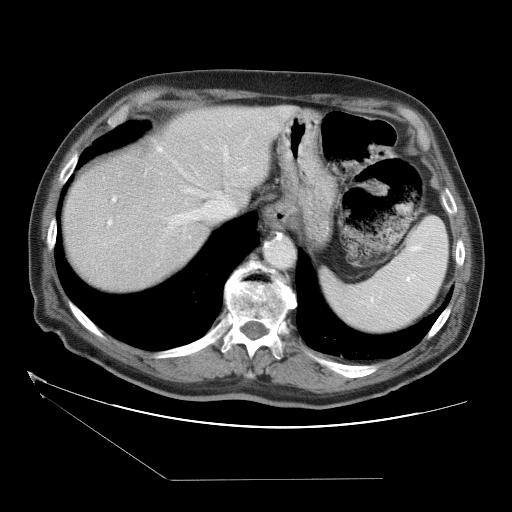
Contrast-enhanced abdominal CT (liver protocol), one axial slice. Slice 28 of 38 in the series (ordered by position). Reconstruction kernel STANDARD. One of 2 acquisitions stored at this slice position. Soft-tissue window (W 400 / L 40 HU). 5 mm slice thickness. 512 × 512 image matrix. Case-level facts recorded for this patient, not image findings: diagnosis: hepatocellular carcinoma (patient treated with transarterial chemoembolisation; whether this scan precedes or follows treatment is not stated here); TNM stage (as recorded): Stage-II; Child-Pugh class: A; tumour nodularity: multinodular.
Outlined on this slice (semi-automatically segmented with operator editing):
- abdominal aorta: bounding box (x1, y1, x2, y2) in pixels: (266, 239, 294, 267)
- liver parenchyma outside the tumour (the mass and vessels are separate outlines, so this box may not span the whole liver): (62, 106, 316, 290)
- liver vessels: (107, 145, 230, 229)